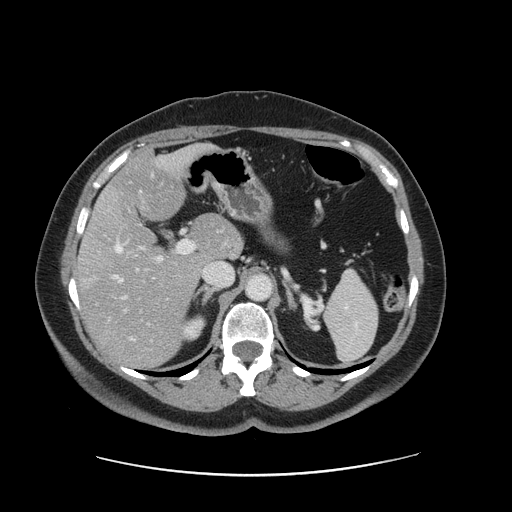
Contrast-enhanced abdominal CT, one axial slice. Slice 88 of 161 in the series (ordered by position). 120 kVp. Intravenous contrast given. Soft-tissue window (W 400 / L 40 HU). 512 × 512 image matrix. Female patient, age 62 years. From the clinical record (not read from this slice): diagnosis: colorectal cancer liver metastases, imaged before liver resection; multiple liver metastases: no; largest metastasis: 2.5 cm; disease in both lobes: no.
Structures marked on this image (outlined manually by an expert reader):
- hepatic veins: bounding box [x1, y1, x2, y2] px = [114, 191, 142, 282]
- liver: [77, 146, 241, 367]
- planned liver remnant (the part of the liver to remain after resection): [109, 145, 241, 264]
- portal vein (with intrahepatic branches): [120, 240, 195, 326]